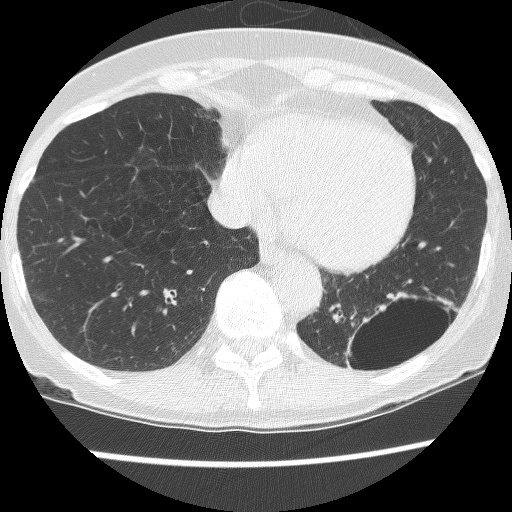
Axial slice from a low-dose chest CT screening exam; third screening round (two years after baseline); lung window (W 1500 / L -600 HU); 2.5 mm slice thickness; slice 93 of 130 in the series. Female participant, aged 61 years at enrolment. Current smoker at enrolment.
Lesion marked by an expert reader, box from (x=333, y=292) to (x=445, y=387) px. The screening reader recorded 2 non-calcified nodules or masses ≥4 mm on this exam (left lower lobe, left lower lobe); which of them this box marks is not recorded. Participant outcome: lung cancer diagnosed 166 days after this screen — non-small cell carcinoma, left lower lobe, poorly differentiated (G3), stage IB (AJCC 6th edition), 100 mm at pathology.